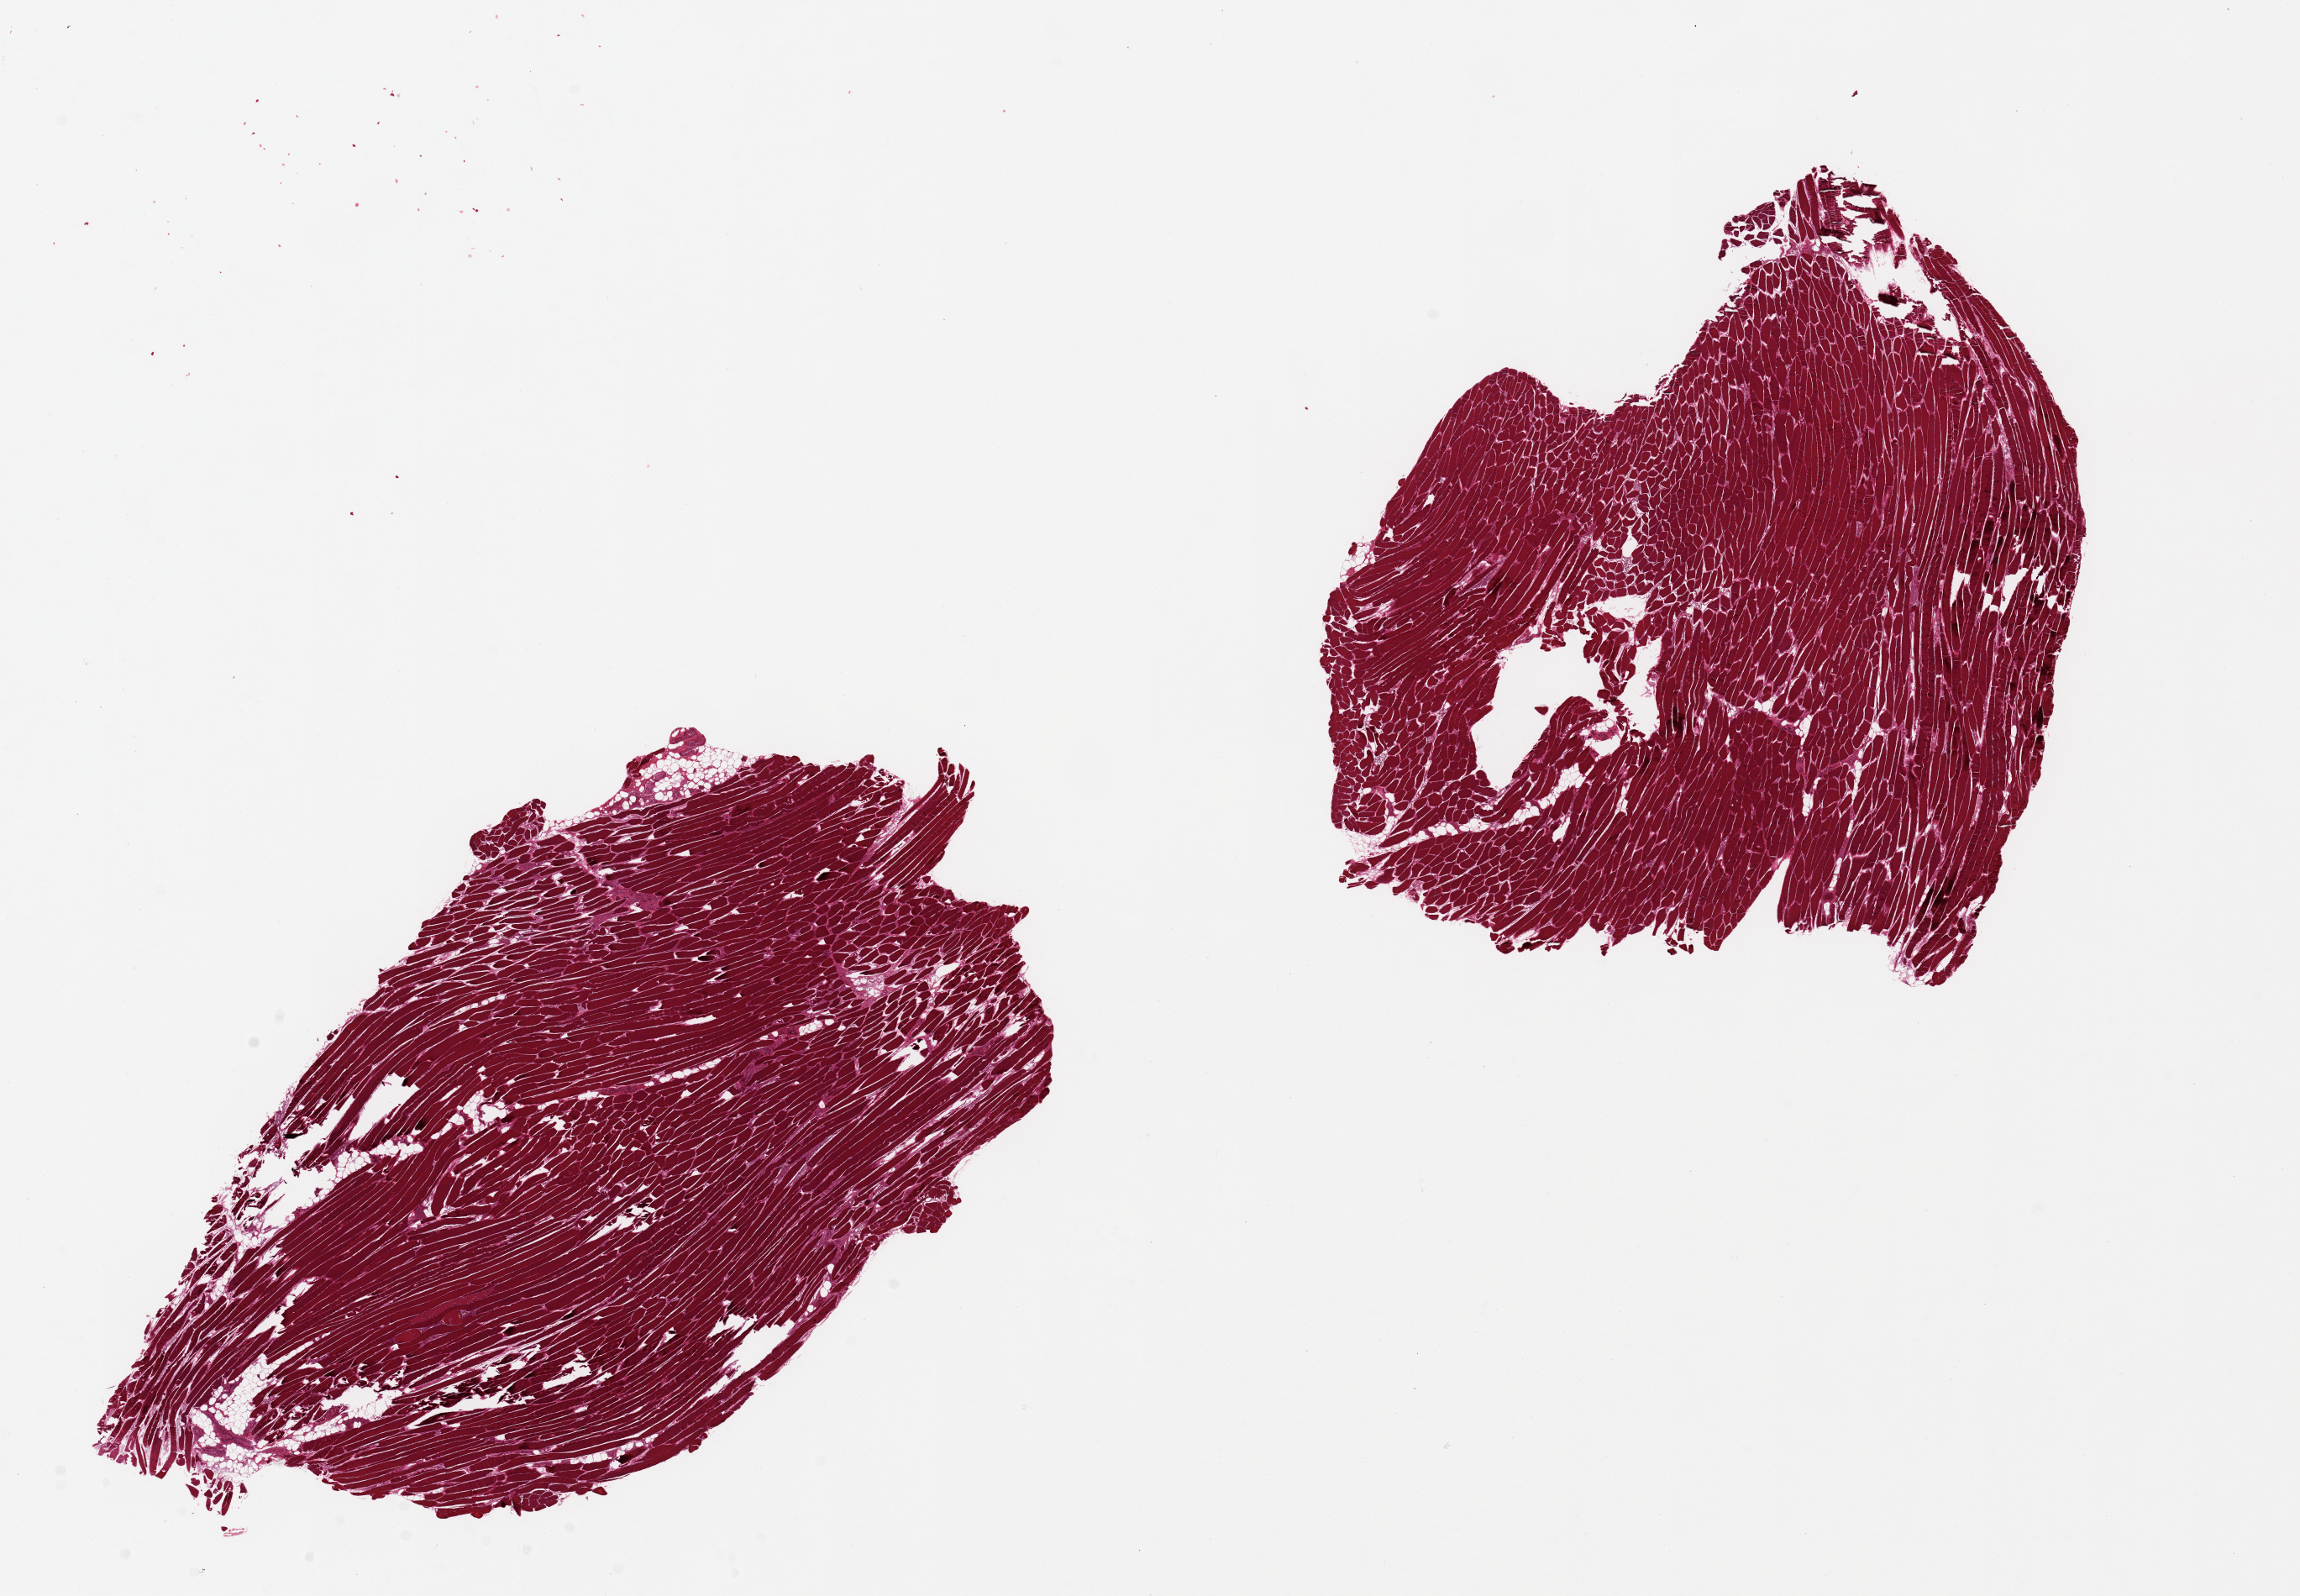
Whole-slide image, hematoxylin and eosin (H&E) stain, a low-resolution overview of the entire scanned area, about 21.7 x 15.0 mm. PAXgene-fixed, paraffin-embedded tissue. Target tissue: skeletal muscle. Donor tissue sample. Male donor.
Pathologist's review note for this sample: 2 alqiuots, ~7x7mm. Minimal interstital fat, unusally poorly preserved.